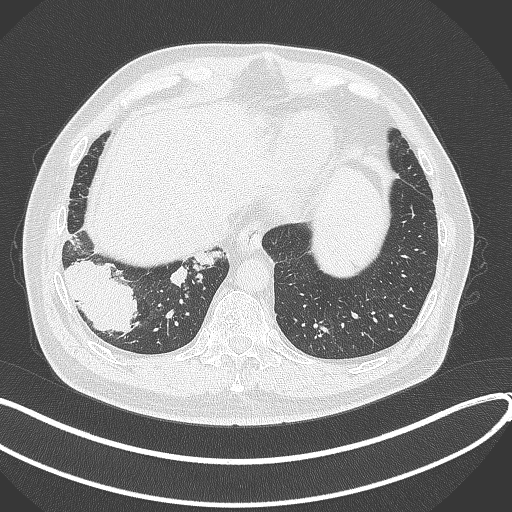
Chest CT, one axial slice; position 71 of 360 along the scan axis; reconstruction kernel B70f; 120 kVp; lung window (W 1500 / L -600 HU); 1 mm slice thickness; 512 × 512 image matrix, field of view 400 × 400 mm. Patient: male, 59 years.
Annotated regions visible in this slice (bounding box drawn by a radiologist):
- lung tumour (recorded histology: adenocarcinoma): bounding box [x1, y1, x2, y2] px = [65, 255, 144, 340]